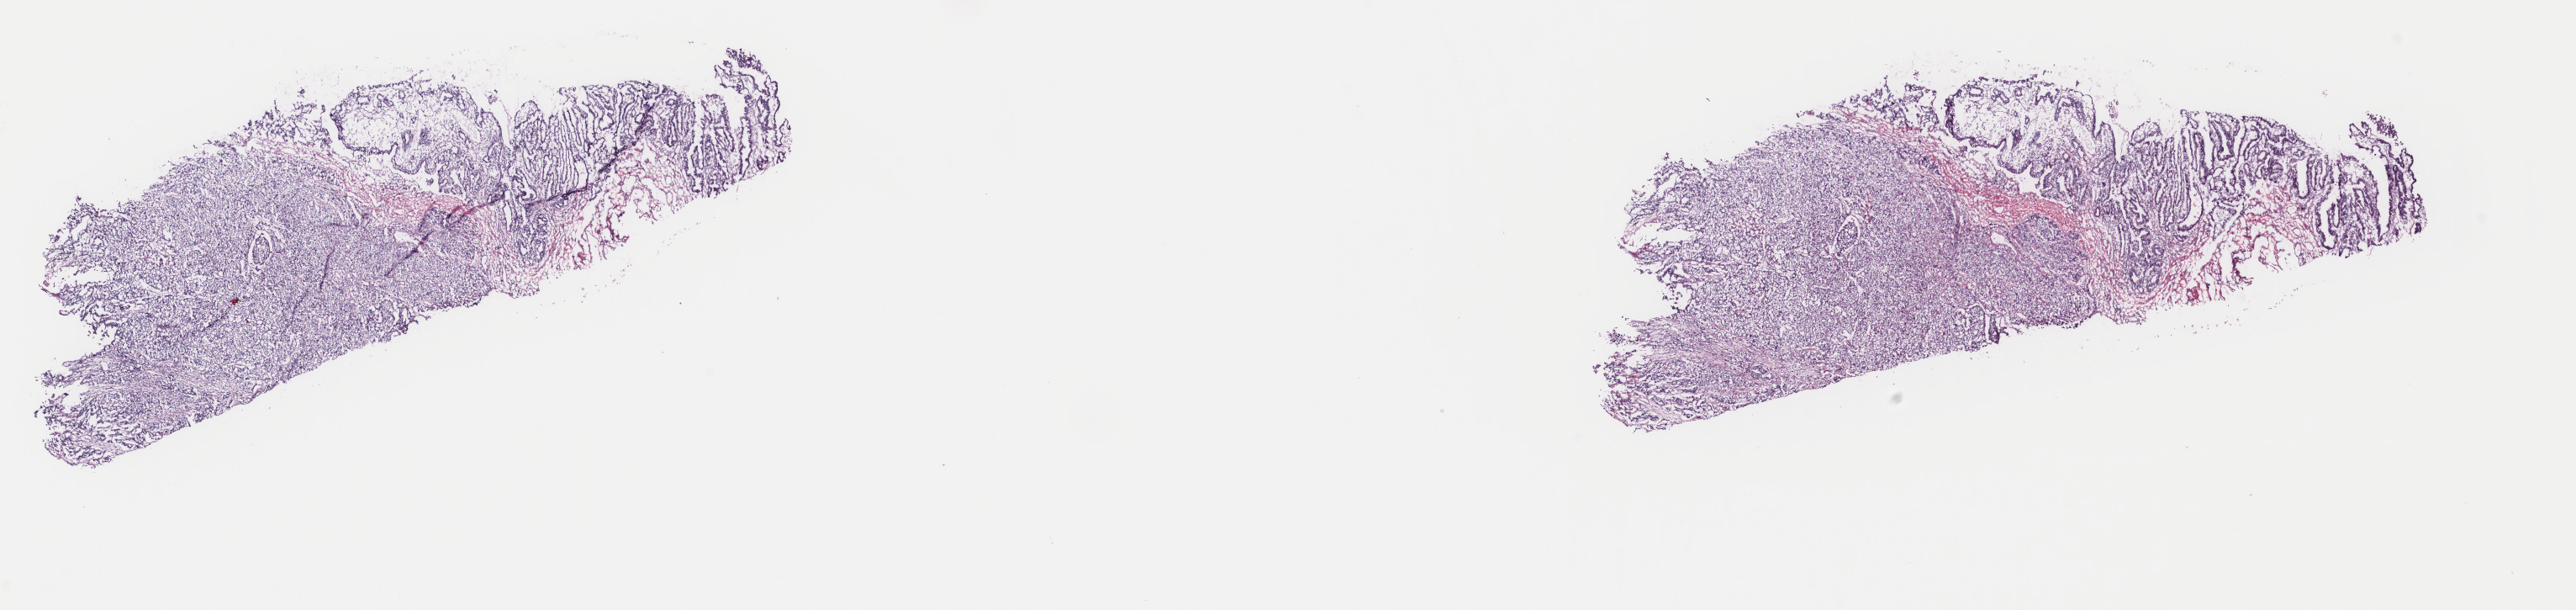
Hematoxylin and eosin (H&E) stained whole-slide image — whole scanned area (about 24.3 x 5.8 mm, slide scanned at 40x) shown as a low-resolution overview. Frozen section from the top of the tissue portion. Primary tumour sample from the stomach. Patient: male, age at initial diagnosis 84 years. Histologic grade: G3 (poorly differentiated). Slide review estimates, as recorded: tumour cells 70%, tumour nuclei 70%, normal cells 5%, stromal cells 25%, necrosis 0%. Inflammatory infiltration, as recorded: lymphocyte infiltration 3%, monocyte infiltration 1%, neutrophil infiltration 5%.
Pathologic diagnosis: Adenocarcinoma, NOS (cardia, NOS).